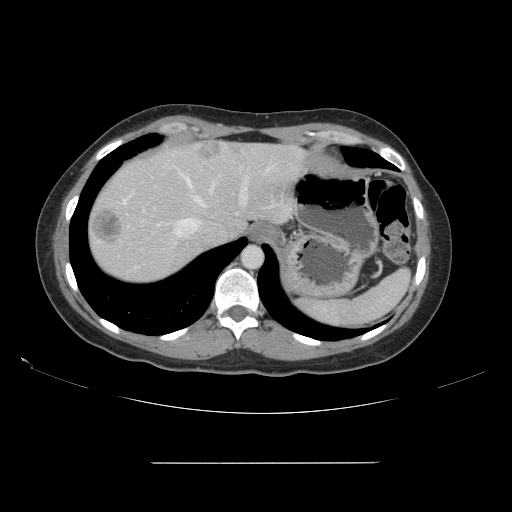
Contrast-enhanced abdominal CT, one axial slice; position 128 of 151 along the scan axis; 120 kVp; intravenous contrast given; soft-tissue window (W 400 / L 40 HU); 2.5 mm slice thickness; 512 × 512 image matrix, field of view 421 × 421 mm. Female patient, age 46 years. Case-level facts recorded for this patient, not image findings: diagnosis: colorectal cancer liver metastases, imaged before liver resection; multiple liver metastases: yes; largest metastasis: 3 cm; chemotherapy before resection: no.
Annotated regions visible in this slice (expert manual segmentation):
- hepatic veins: bounding box (x1, y1, x2, y2) in pixels: (123, 174, 248, 238)
- liver: (88, 142, 301, 283)
- planned liver remnant (the part of the liver to remain after resection): (99, 143, 302, 242)
- liver metastasis: (93, 210, 123, 244)
- liver metastasis: (199, 145, 221, 160)